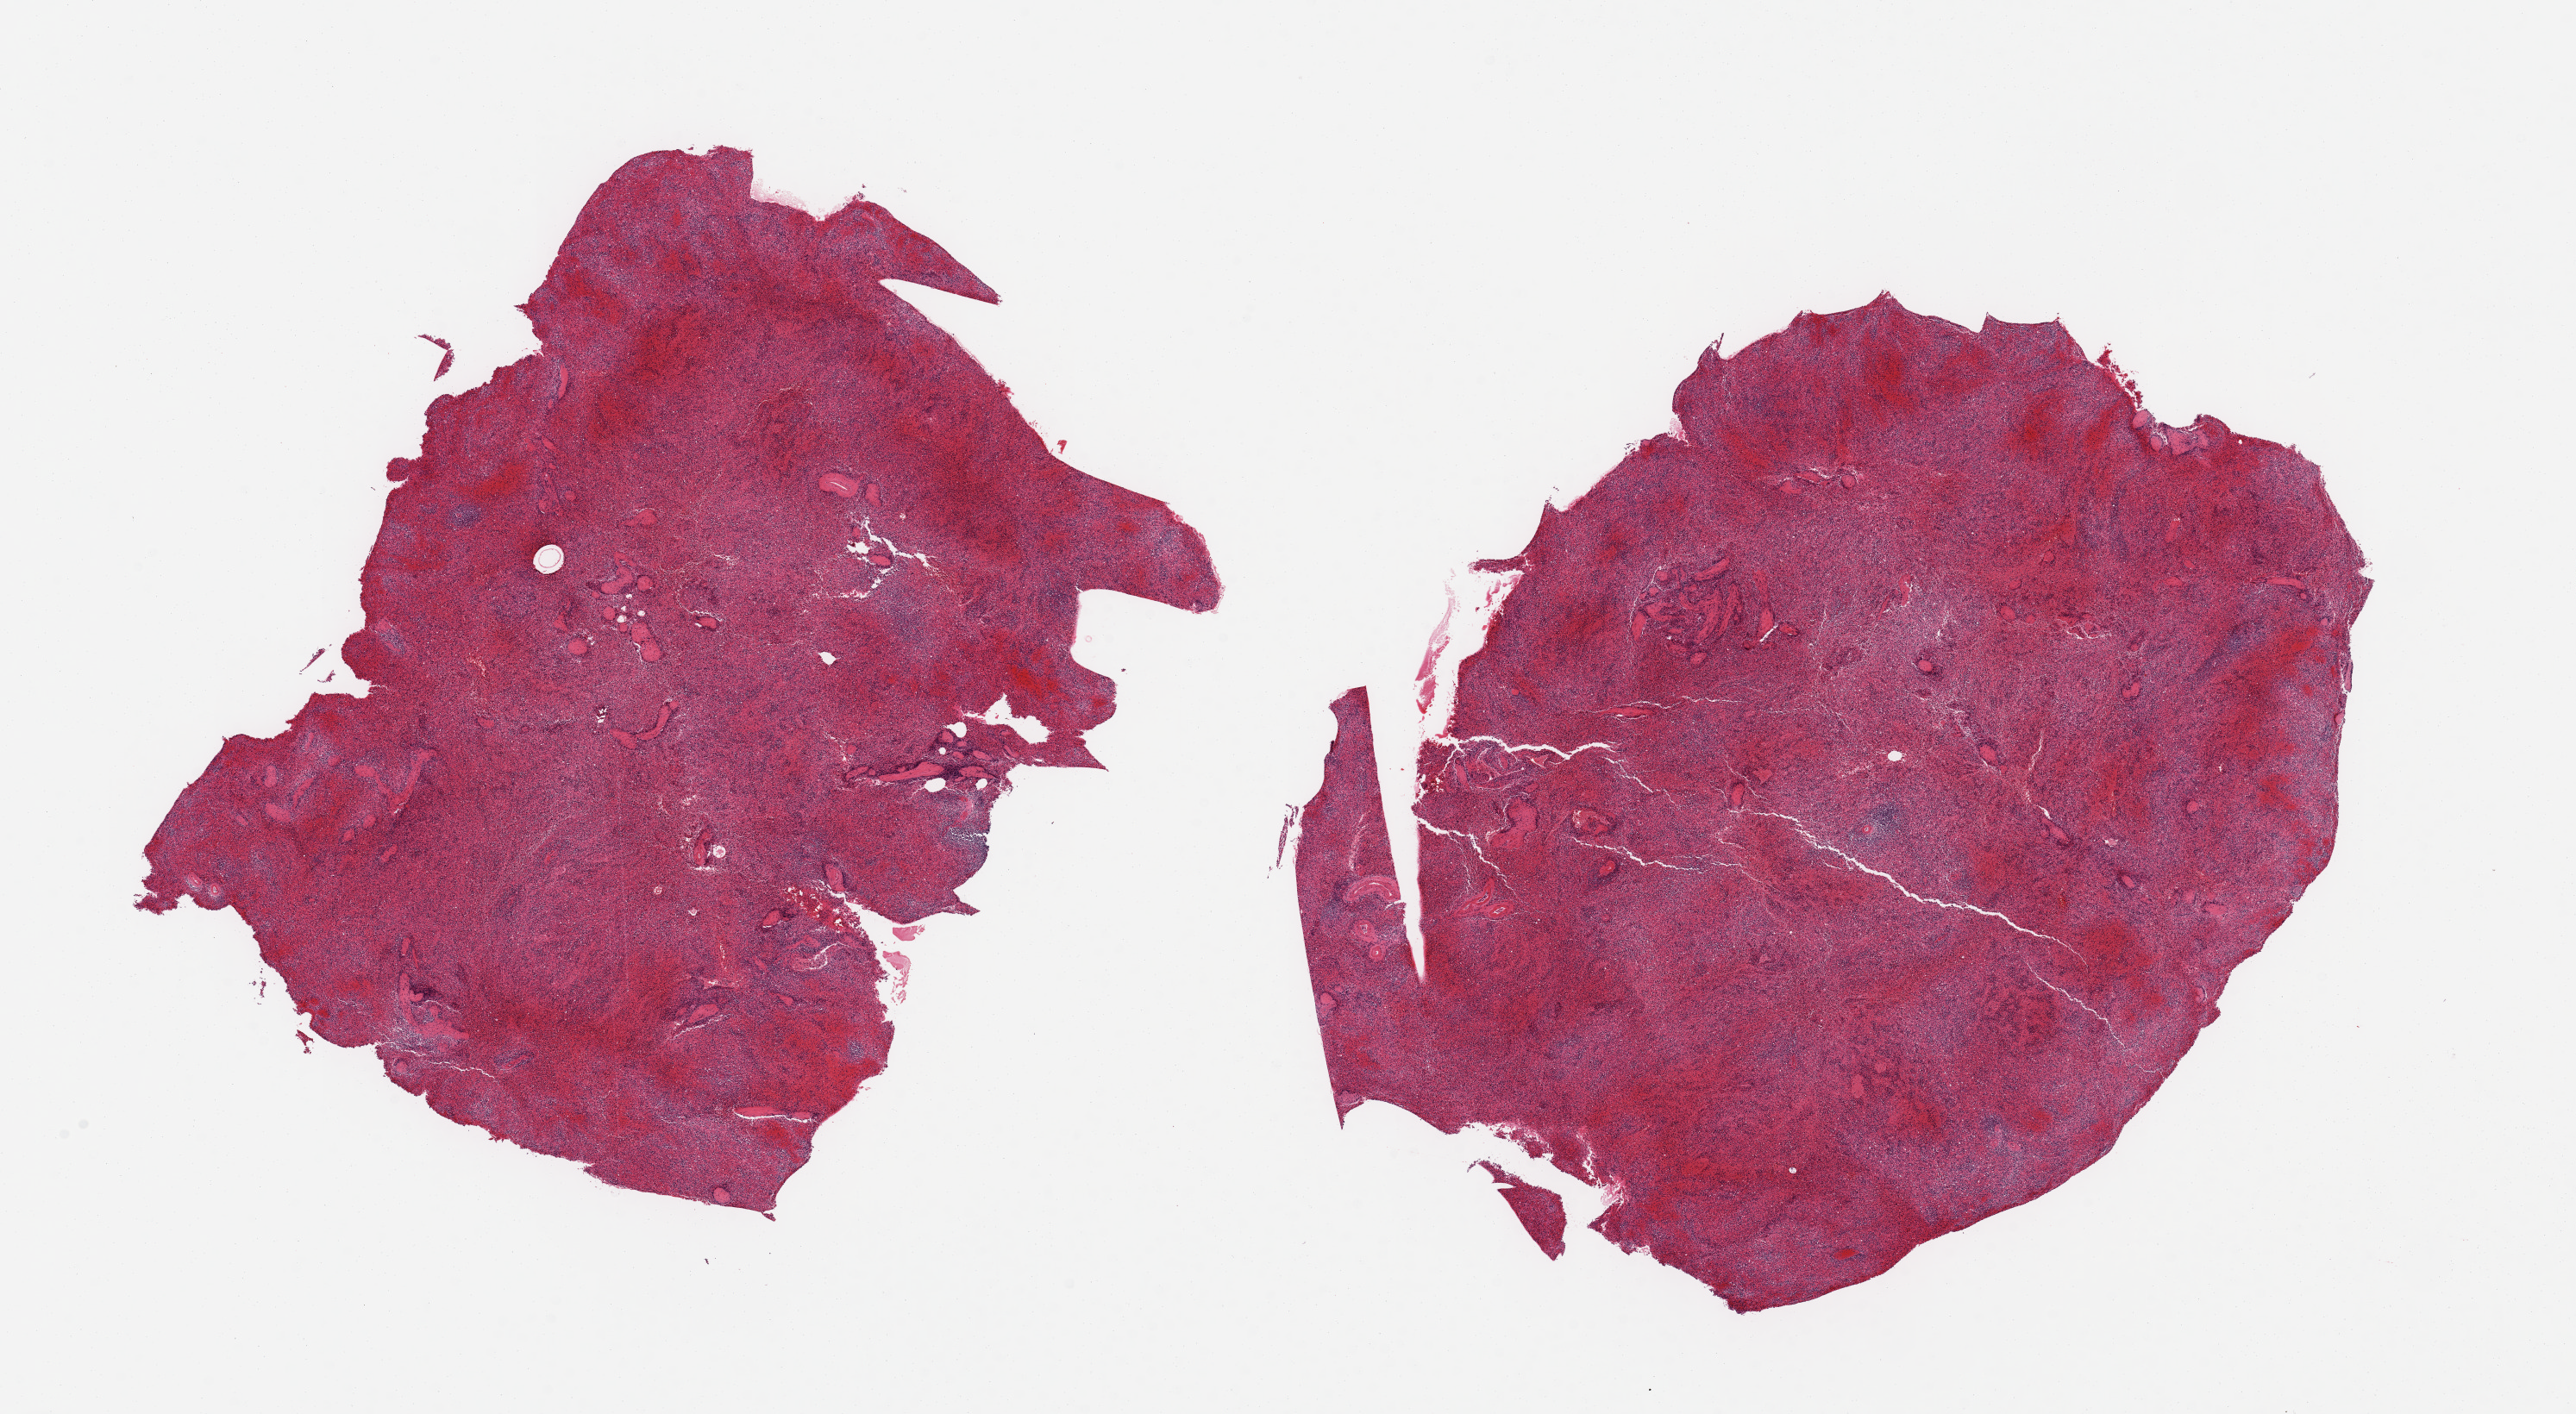
Digitized haematoxylin and eosin-stained section — a low-resolution overview of the entire scanned area, about 23.6 x 13.0 mm, PAXgene-fixed paraffin-embedded (PFPE) section, sampled site (target tissue): spleen, donor tissue sample. Male donor.
Reviewer comment on this tissue sample: 2 pieces, moderate congestion.